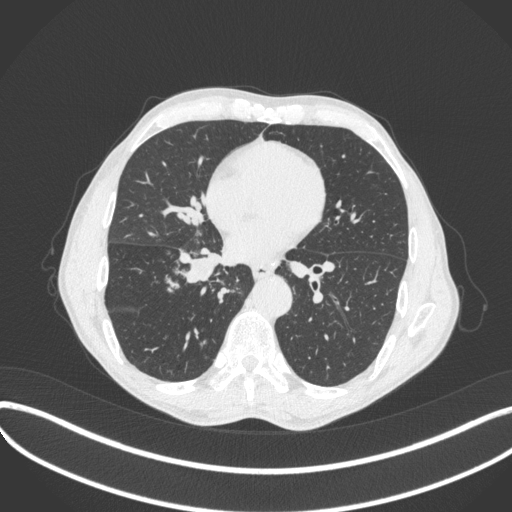
Chest CT, one axial slice. Position 190 of 481 along the scan axis. Reconstruction kernel B31f. 120 kVp. Lung window (W 1500 / L -600 HU). 1 mm slice thickness. 512 × 512 image matrix. Male patient, age 65 years. From the clinical record (not read from this slice): clinical TNM (as recorded): T2a N0 M0; histopathological grade: G2.
Structures marked on this image (rectangle marked by the reading radiologist):
- lung tumour (recorded histology: squamous cell carcinoma): box from (x=178, y=249) to (x=224, y=284) px